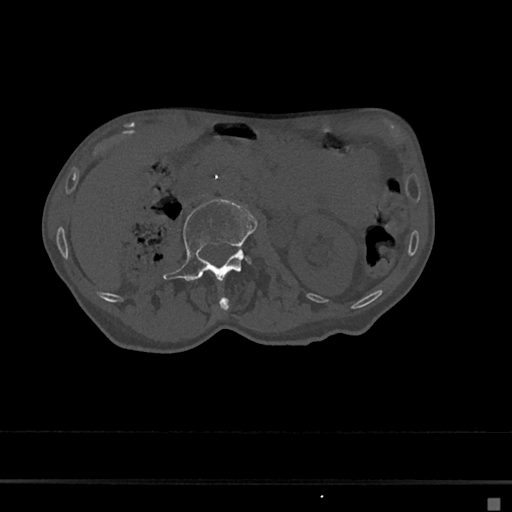
CT including the spine, one axial slice. Position 16 of 797 along the scan axis. Reconstruction kernel Br40s/3. 120 kVp. Bone window (W 1800 / L 400 HU). 0.5 mm slice thickness. 512 × 512 image matrix, field of view 360 × 360 mm. Female patient, age 68 years. Case-level facts recorded for this patient, not image findings: primary cancer: renal.
Structures marked on this image (semi-automatic segmentation, software-assisted and operator-edited):
- L1 vertebra: bounding box [x1, y1, x2, y2] px = [216, 297, 229, 317]
- L2 vertebra: [163, 199, 256, 284]